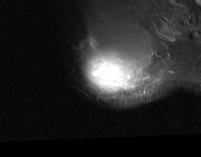
MRI of an extremity soft-tissue mass, one axial slice; position 58 of 74 along the scan axis; STIR; MR volume resampled by the dataset authors to the PET/CT grid (not the native acquisition matrix); 3.27 mm slice thickness; 201 × 157 image matrix, field of view 196 × 153 mm. Male patient. Case-level facts recorded for this patient, not image findings: histological type: pleiomorphic spindle cell undifferentiated; grade: high; site of the primary tumour: right parascapusular.
Annotated regions visible in this slice (expert contour drawn on MRI and transferred to this co-registered scan by the dataset authors):
- gross tumour volume including surrounding oedema: box from (x=88, y=57) to (x=148, y=92) px
- gross tumour volume (mass): (x=90, y=57)–(x=123, y=88)